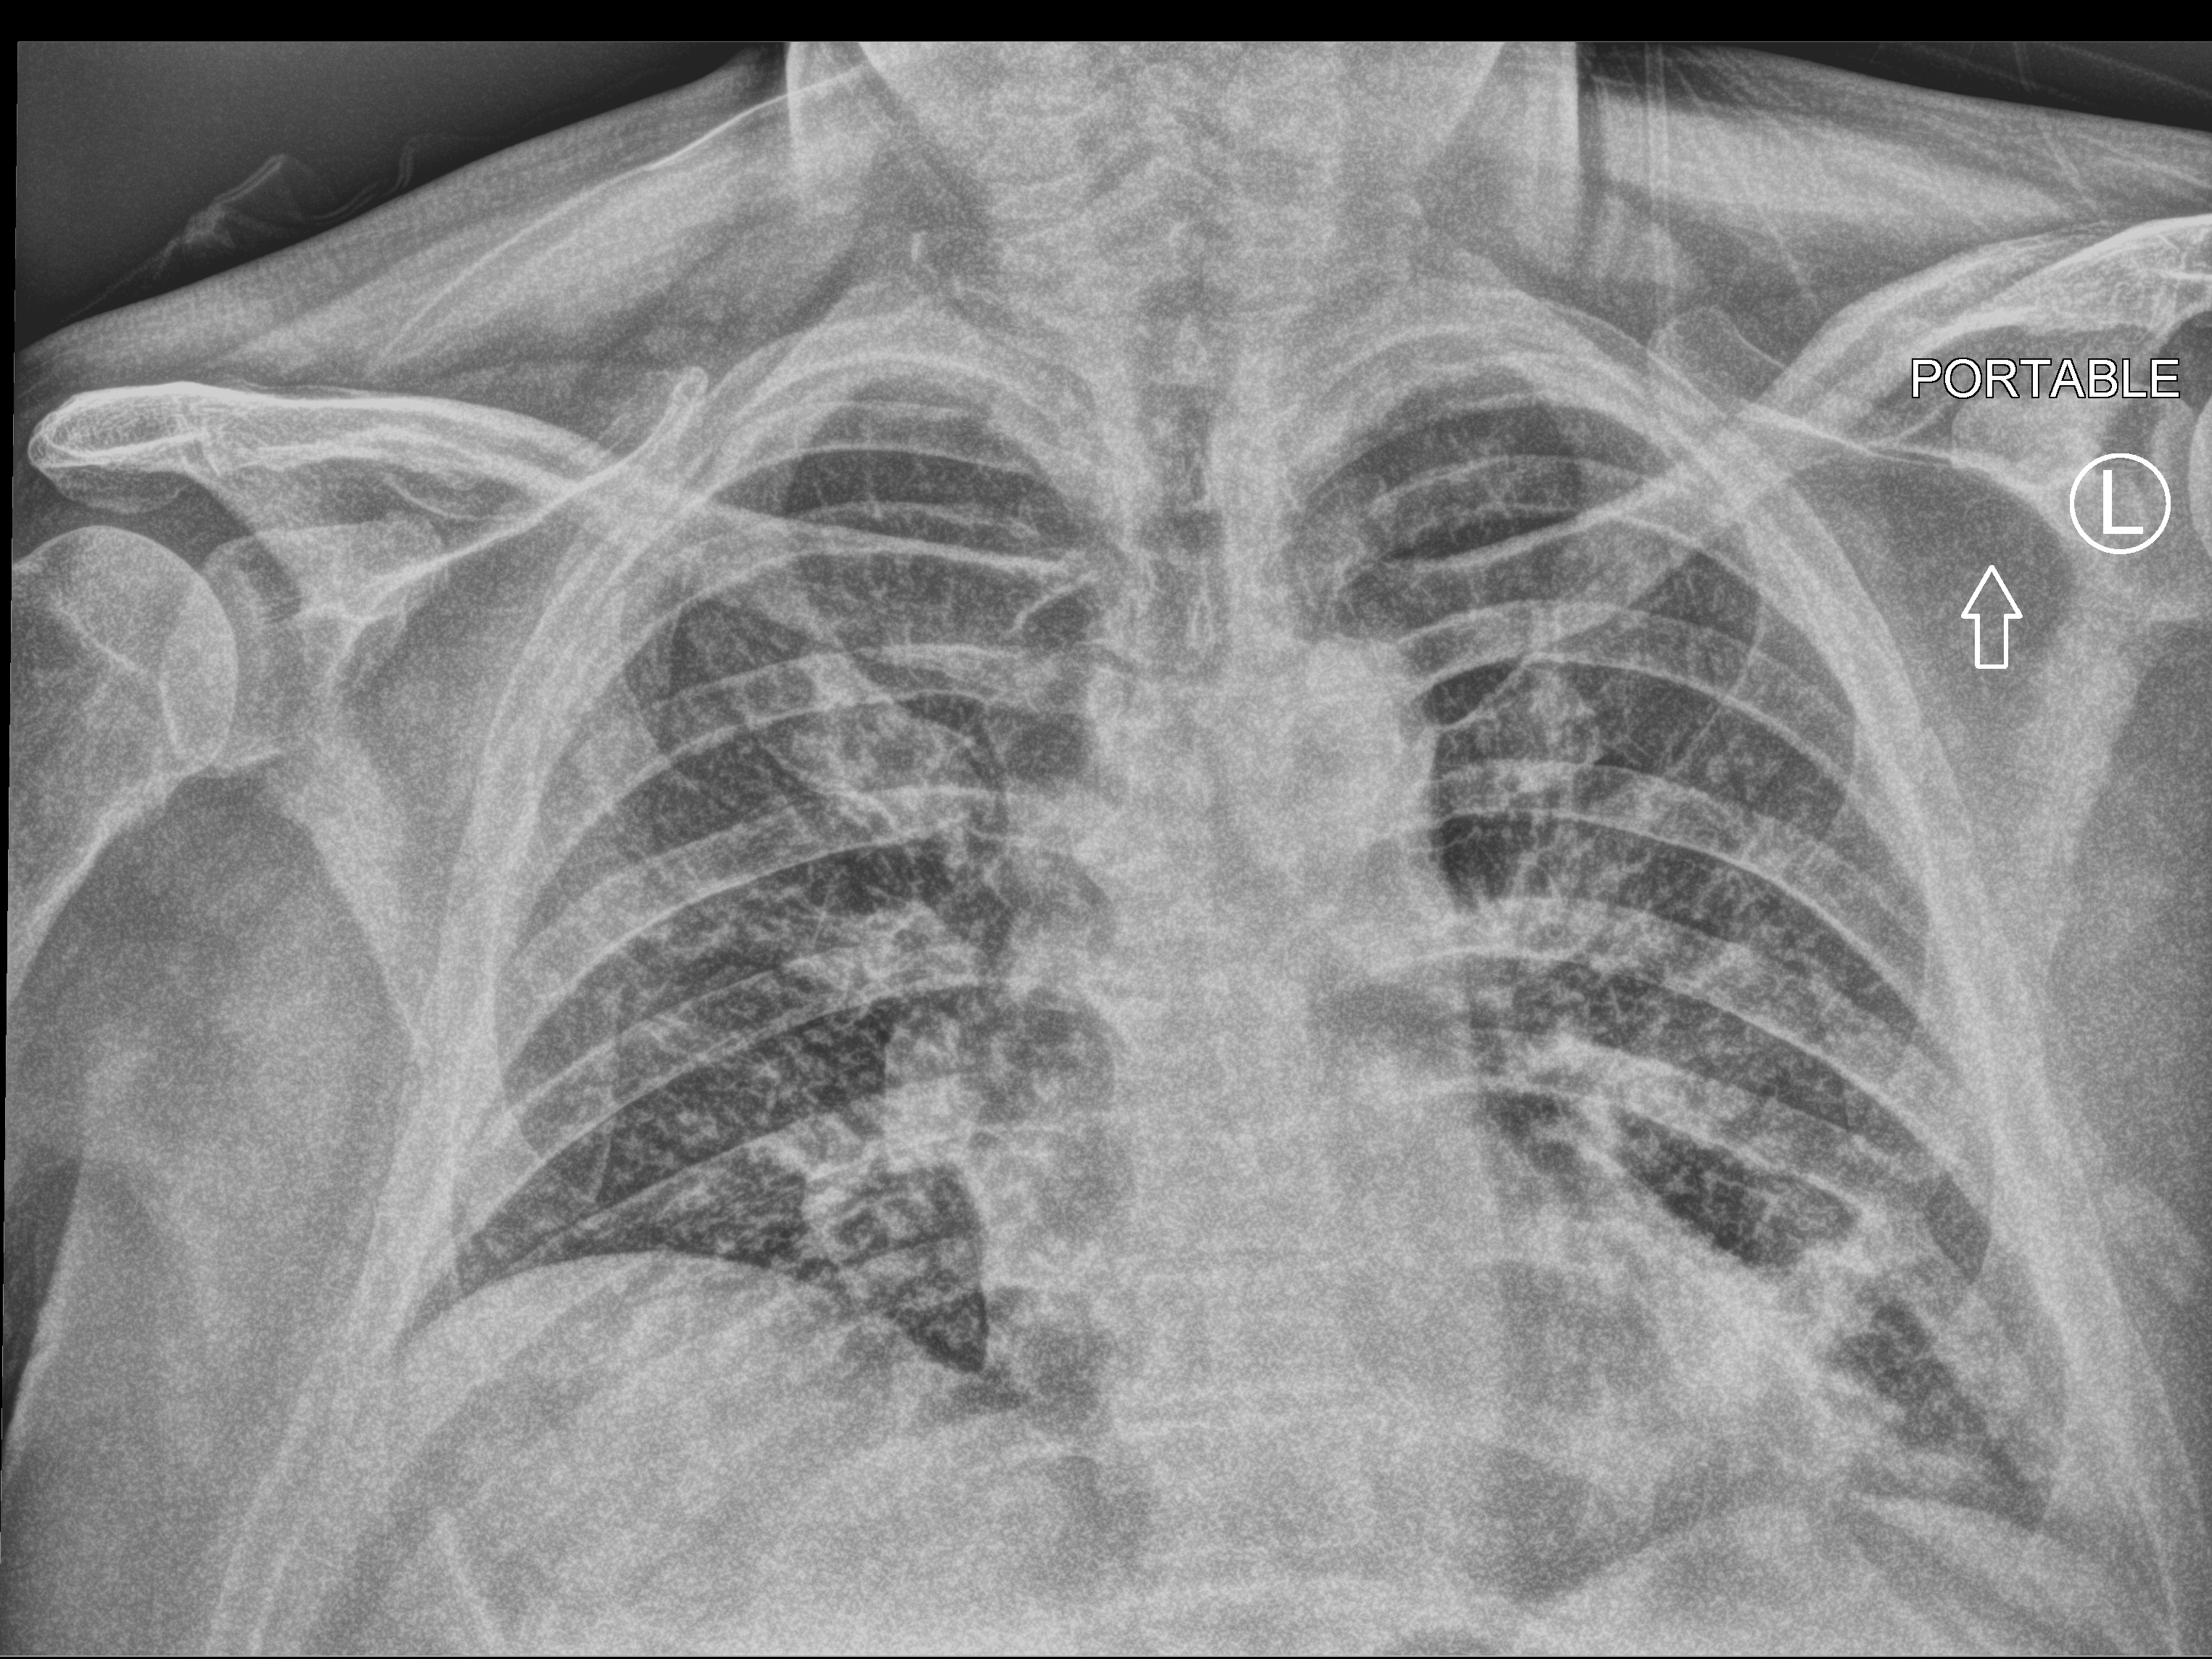
Chest X-ray (portable), anteroposterior (AP) projection. Patient hospitalised with COVID-19; male, aged 60–74 years.
From the hospital-stay record, not from the radiograph (when in the stay this image was taken is not recorded):
- COPD (admission record): yes
- mechanically ventilated during this hospital stay: no